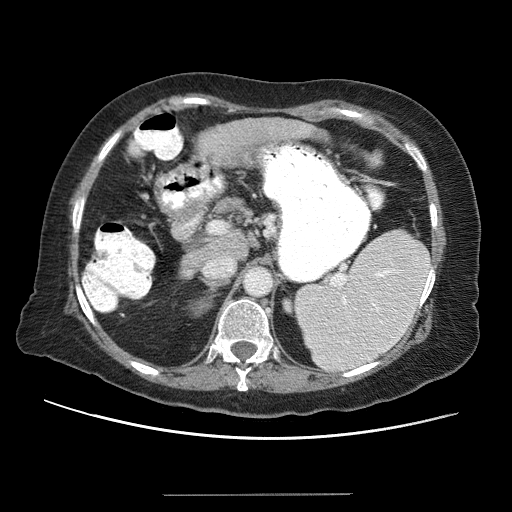
Contrast-enhanced abdominal CT (liver protocol), one axial slice. 120 kVp. Soft-tissue window (W 400 / L 40 HU). 2.5 mm slice thickness. 512 × 512 image matrix, field of view 380 × 380 mm. Case-level facts recorded for this patient, not image findings: diagnosis: hepatocellular carcinoma (patient treated with transarterial chemoembolisation; whether this scan precedes or follows treatment is not stated here); TNM stage (as recorded): Stage-IIIB; Child-Pugh class: A; tumour differentiation: moderately differentiated.
Outlined on this slice (semi-automatically segmented with operator editing):
- liver parenchyma outside the tumour (the mass and vessels are separate outlines, so this box may not span the whole liver): bounding box [x1, y1, x2, y2] px = [179, 118, 316, 276]
- liver vessels: [208, 138, 241, 254]